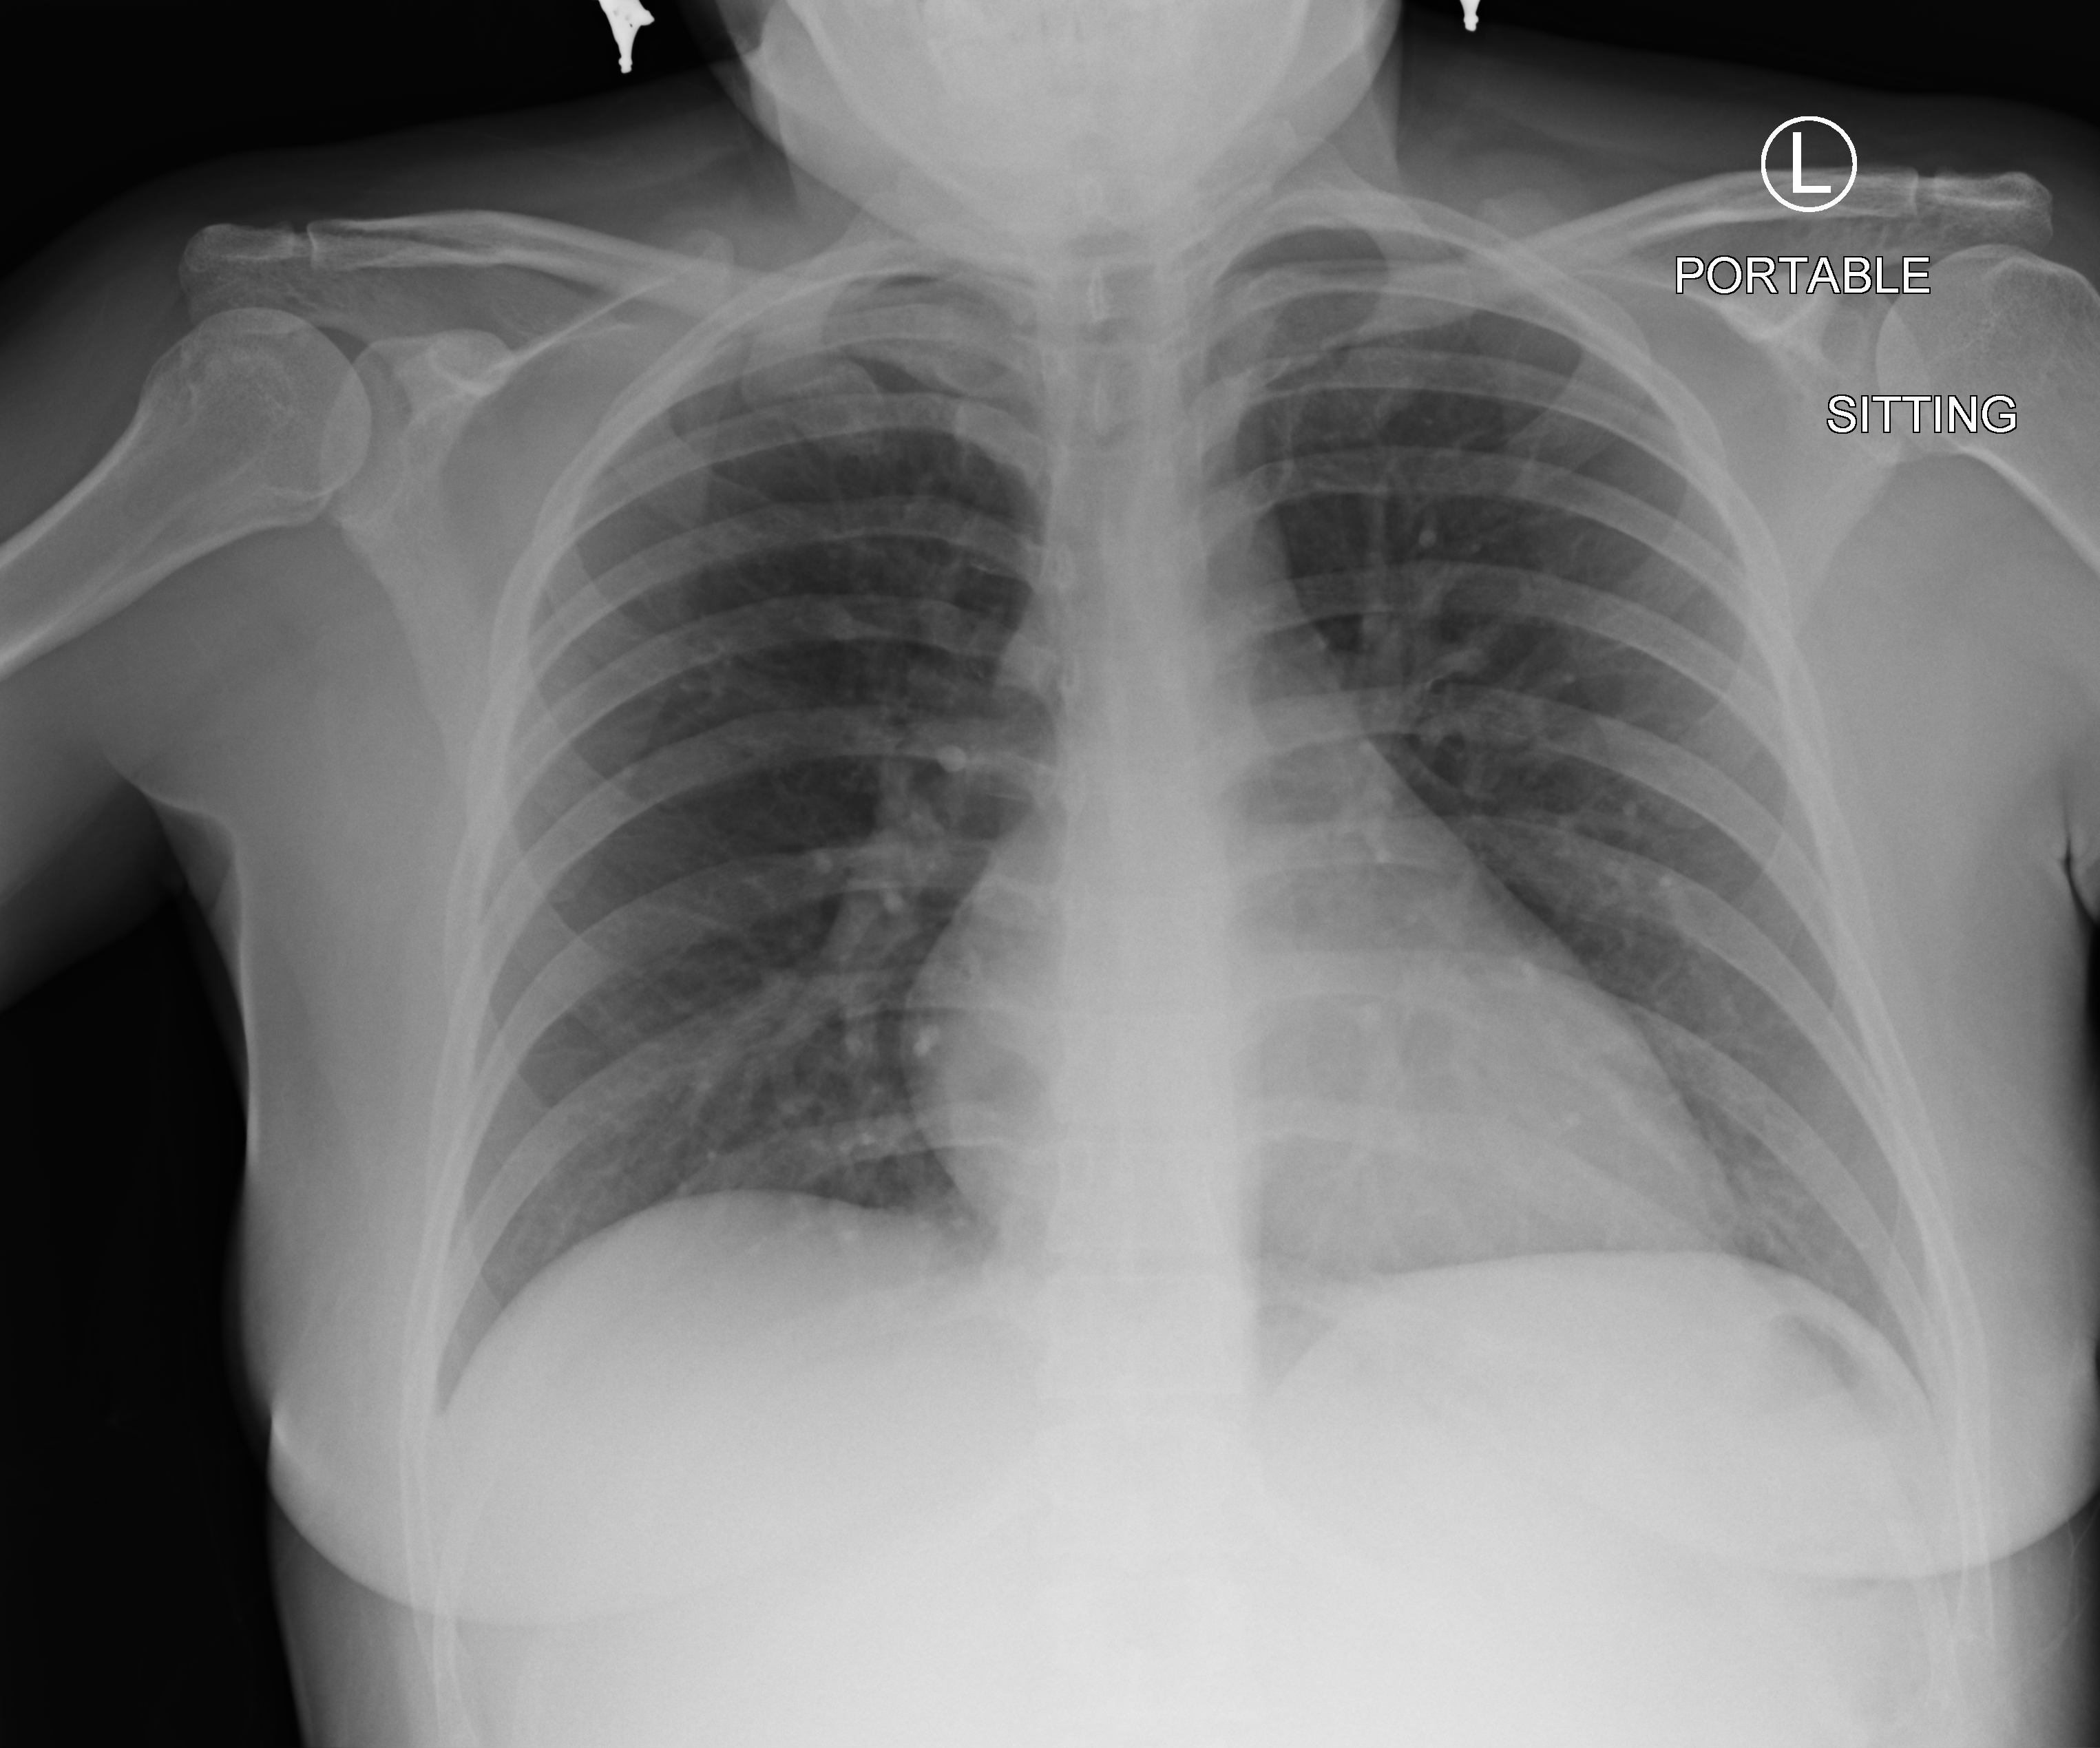
Chest X-ray (portable); anteroposterior (AP) projection. Patient hospitalised with COVID-19; female, aged 18–59 years.
Admission-level facts for this patient (not findings on this image; timing relative to this image not recorded): mechanically ventilated during this hospital stay: no; length of hospital stay: 2 days; smoking status (admission record): never.